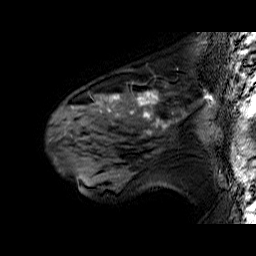
Breast MRI (dynamic contrast-enhanced), one sagittal slice. Dynamic contrast-enhanced series, time point 2 of 6 at this slice position (early post-contrast). 1.5 T. TE 6.4 ms, TR 32.9 ms. 256 × 256 image matrix. Female patient. From the clinical record (not read from this slice): setting: breast cancer imaged before/during neoadjuvant chemotherapy; receptor status: HER2-positive.
Annotated regions visible in this slice (semi-automatic segmentation, software-assisted and operator-edited):
- analysis volume of interest (the breast-tissue region the enhancement analysis was run in; not a lesion): bounding box (x1, y1, x2, y2) in pixels: (51, 80, 192, 160)
- tumour enhancement mask (voxels above the 100 % enhancement threshold inside the analysis volume of interest): (98, 91, 158, 134)